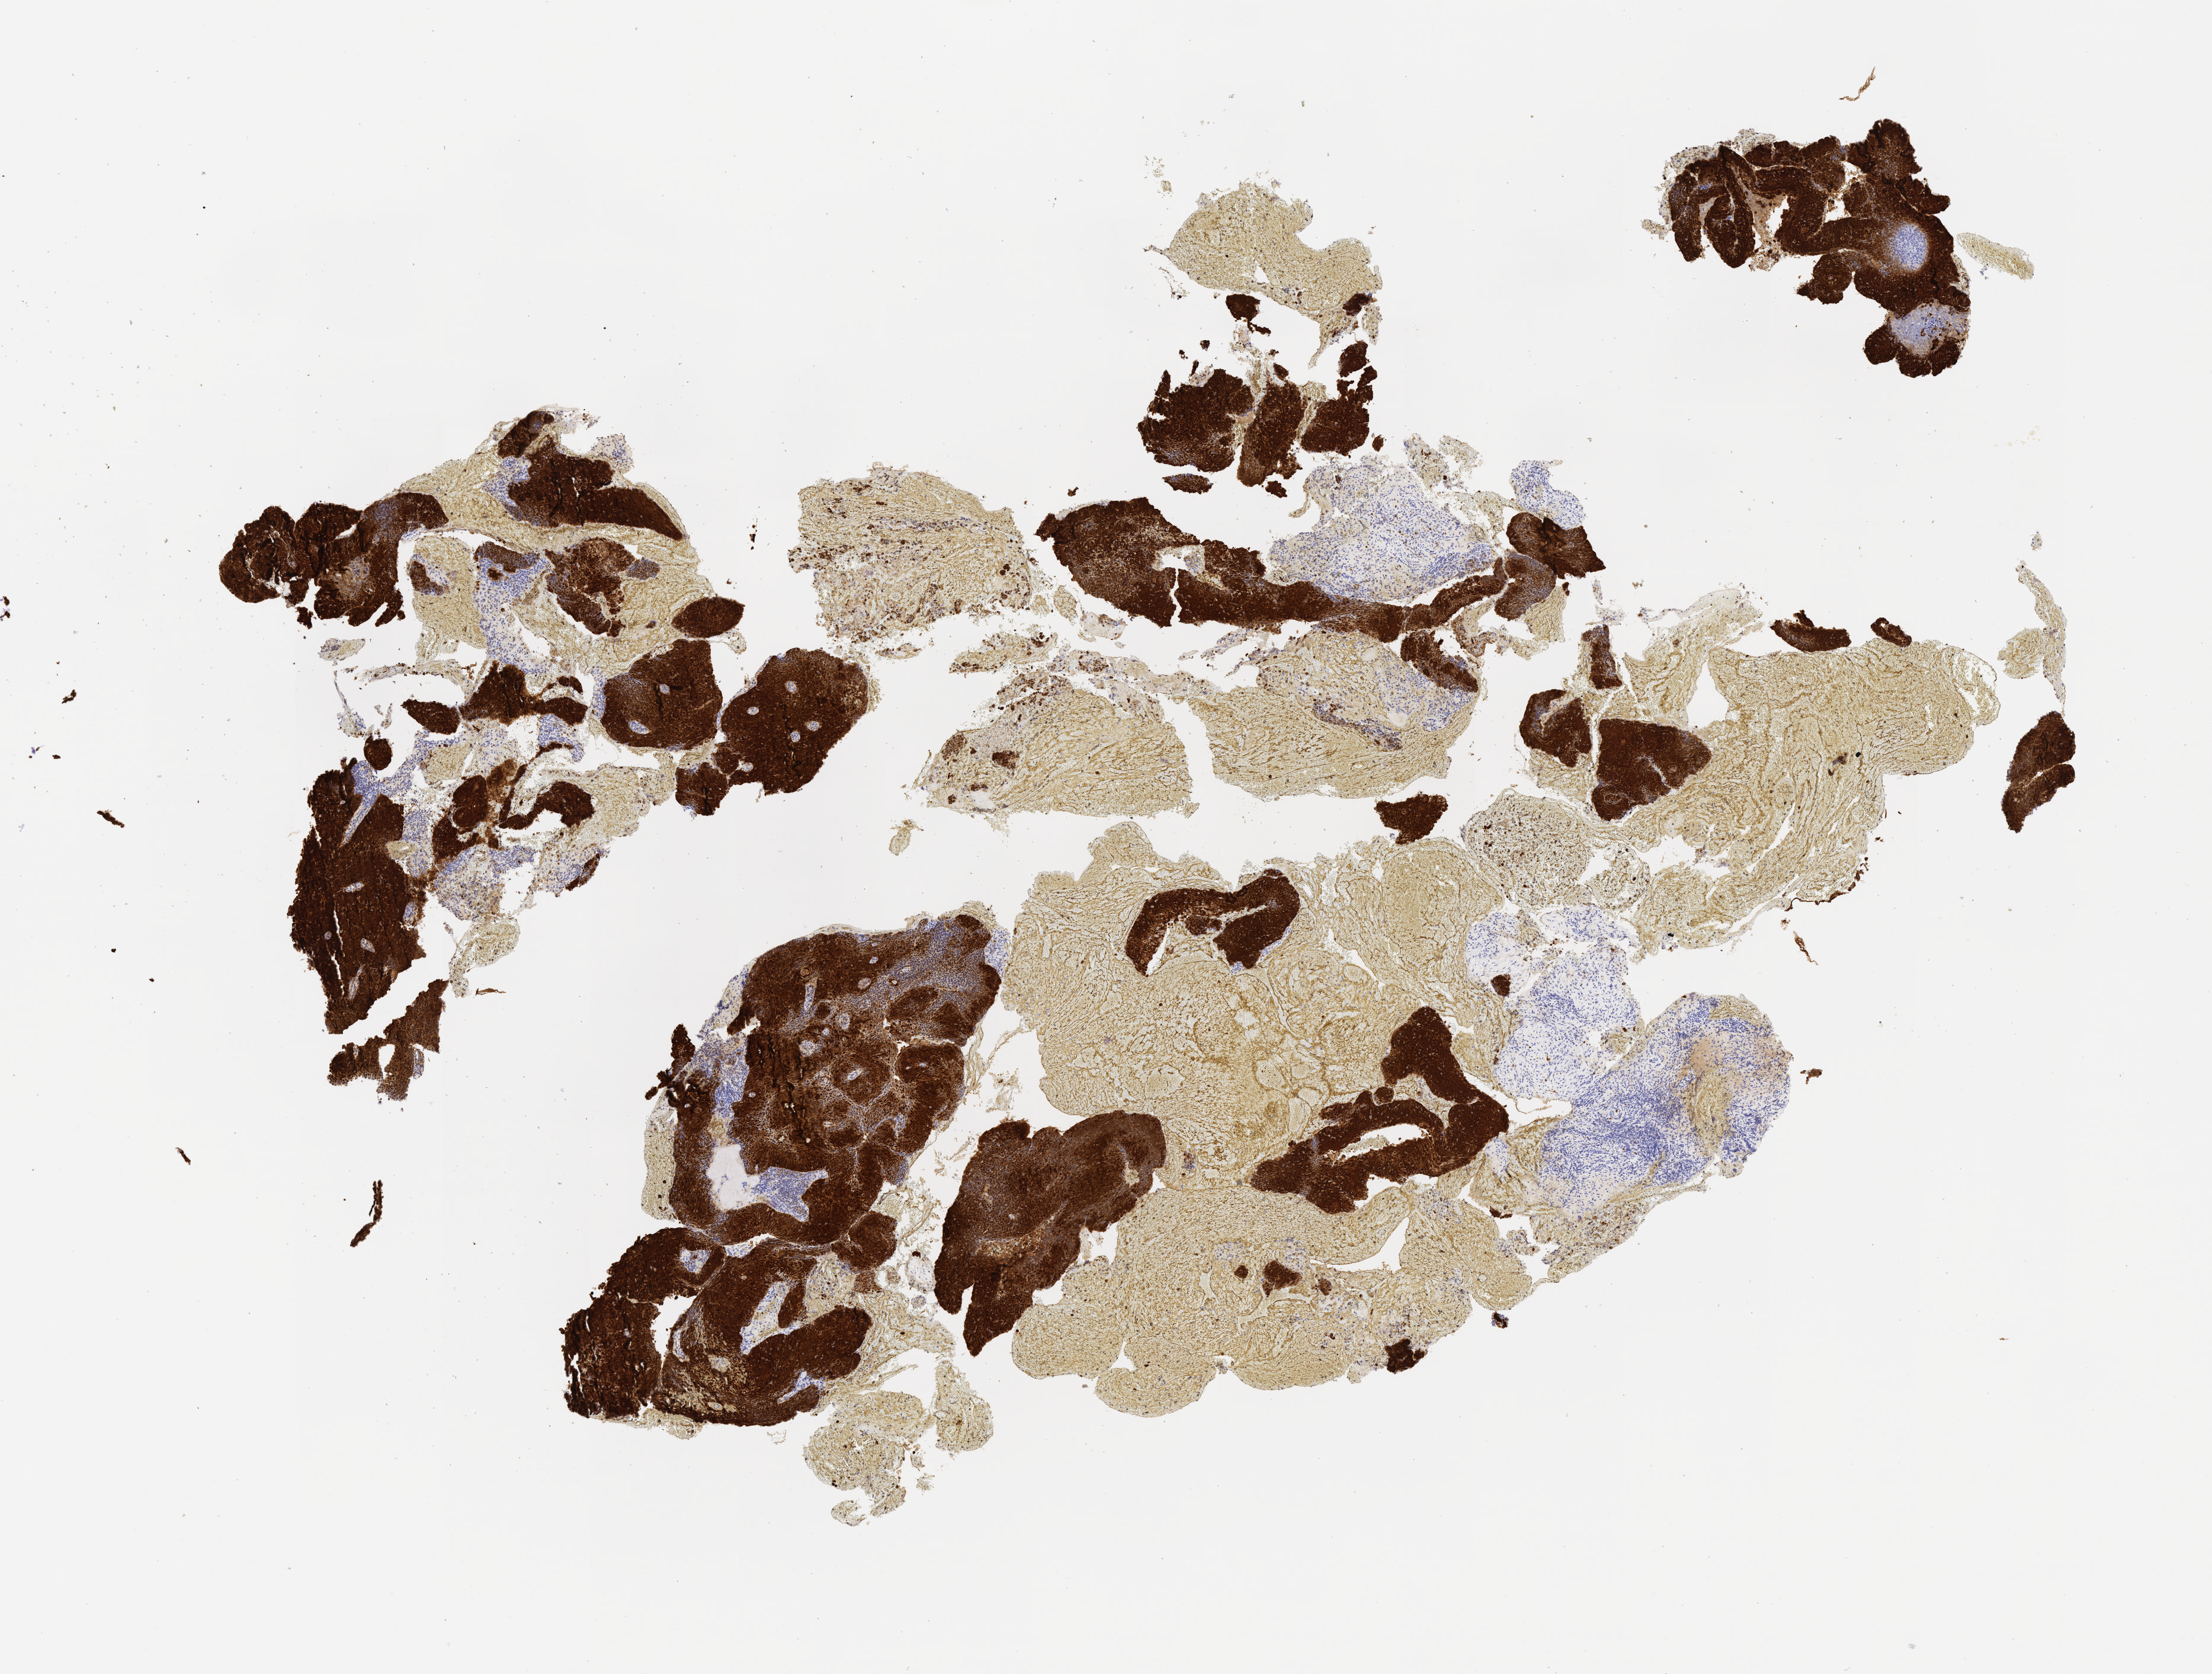
IHC for p16 (p16INK4a), whole-slide image, shown as a low-resolution overview of the whole scanned area (about 7.5 x 5.7 mm). Tumor tissue. Site: cervix. Patient female; age 50 years.
• diagnosis: Squamous cell carcinoma, large cell, nonkeratinizing, NOS